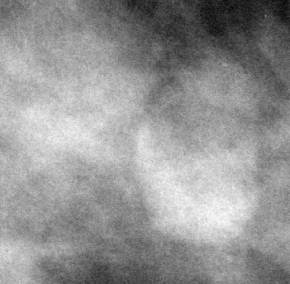
Cropped region of a digitized screen-film mammogram centred on a radiologist-marked abnormality; left breast; CC view.
Marked abnormality: mass, shape lobulated, margins circumscribed; BI-RADS assessment category 3; pathology result (as recorded, not read from the image): benign.